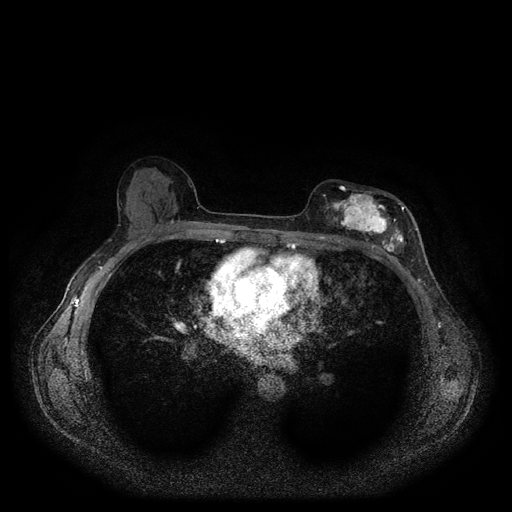
Breast MRI (dynamic contrast-enhanced, multi-phase), one axial slice; slice 59 of 116 in the series (ordered by position); dynamic contrast-enhanced series, time point 2 of 5 at this slice position (early post-contrast); 1.5 T; TE 2.6 ms, TR 5.3 ms; 512 × 512 image matrix, field of view 350 × 350 mm. Female patient, age 51 years.
Outlined on this slice (semi-automatic segmentation, software-assisted and operator-edited):
- breast lesion (labelled 'tumour' in the annotation; benign lesions carry a separate 'benign' label): bounding box [x1, y1, x2, y2] px = [320, 187, 408, 257]